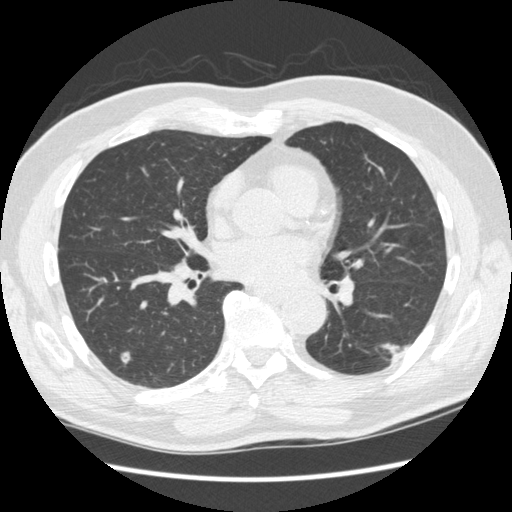
Low-dose screening chest CT, axial slice. Baseline annual screen. Lung window (W 1500 / L -600 HU). 1.25 mm slice thickness. 120 kVp. 512 × 512 image matrix, field of view 360 × 360 mm. Male participant, aged 74 years at enrolment. Former smoker at enrolment.
- Lesion marked by an expert reader, bounding box <376,324,418,375> (left, top, right, bottom; pixels).
- The screening reader recorded 3 non-calcified nodules or masses ≥4 mm on this exam (right upper lobe, right lower lobe, left upper lobe); which of them this box marks is not recorded.
- Later outcome: lung cancer diagnosed 384 days after this screen (after the second annual screen) — squamous cell carcinoma, NOS, left lower lobe, well differentiated (G1), stage IA (AJCC 6th edition), 28 mm at pathology.